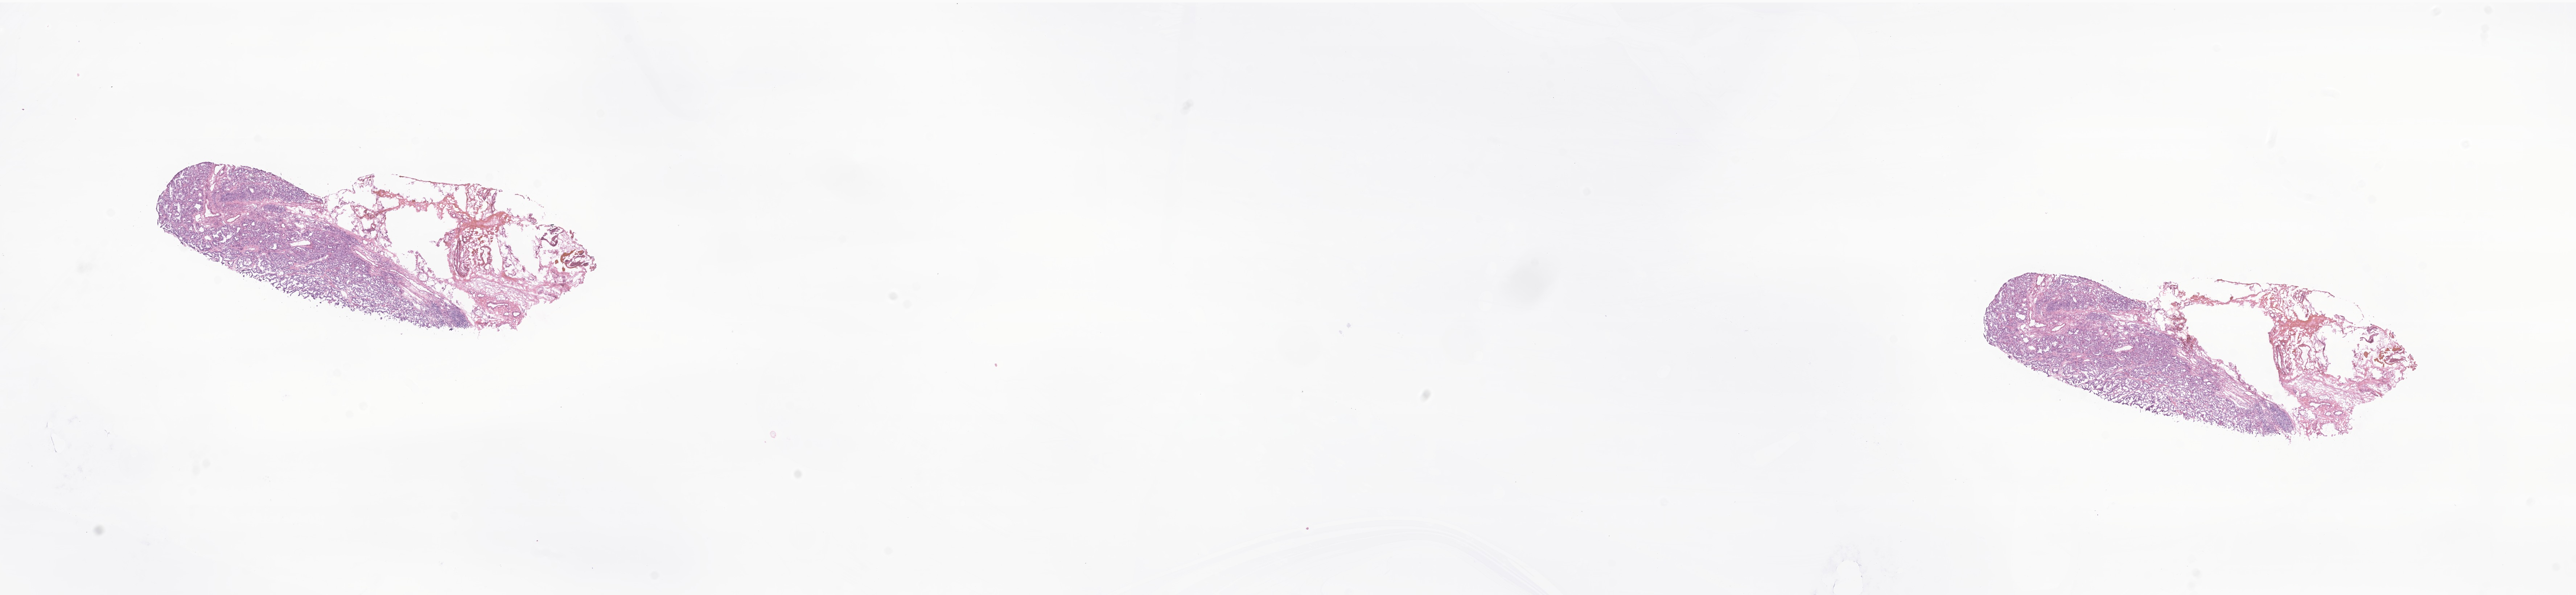
Whole-slide image, haematoxylin and eosin stain of tumor tissue from the thyroid — whole scanned area (about 29.9 x 6.9 mm) shown as a low-resolution overview, frozen section. Patient male; age 171 months.
Diagnosis: Papillary carcinoma, NOS.